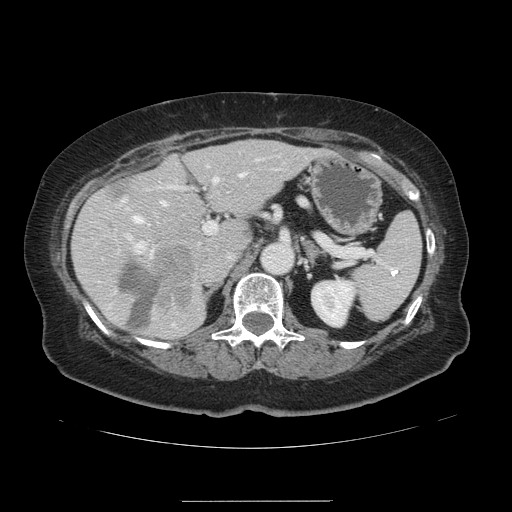
Contrast-enhanced abdominal CT, one axial slice. Slice 78 of 141 in the series (ordered by position). Intravenous contrast given. Soft-tissue window (W 400 / L 40 HU). 512 × 512 image matrix, field of view 393 × 393 mm. Female patient, age 74 years. Case-level facts recorded for this patient, not image findings: diagnosis: colorectal cancer liver metastases, imaged before liver resection; multiple liver metastases: yes; largest metastasis: 7 cm.
Structures marked on this image (expert manual segmentation):
- hepatic veins: bounding box [x1, y1, x2, y2] px = [131, 173, 244, 226]
- liver: [74, 140, 321, 340]
- planned liver remnant (the part of the liver to remain after resection): [74, 140, 321, 339]
- portal vein (with intrahepatic branches): [126, 158, 260, 256]
- liver metastasis: [104, 181, 134, 203]
- liver metastasis: [120, 262, 162, 332]
- liver metastasis: [151, 245, 195, 307]